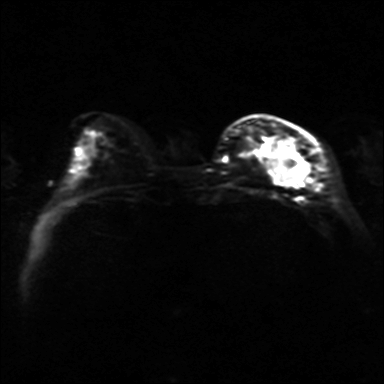
Breast MRI, one axial slice; slice 10 of 36 in the series (ordered by position); diffusion-weighted series; image 2 of 4 stored at this slice position (different b-values; order by instance number); 3 T; 384 × 384 image matrix. Female patient.
Structures marked on this image (outlined manually by an expert reader):
- tumour on diffusion-weighted imaging: bounding box [x1, y1, x2, y2] px = [274, 152, 303, 183]